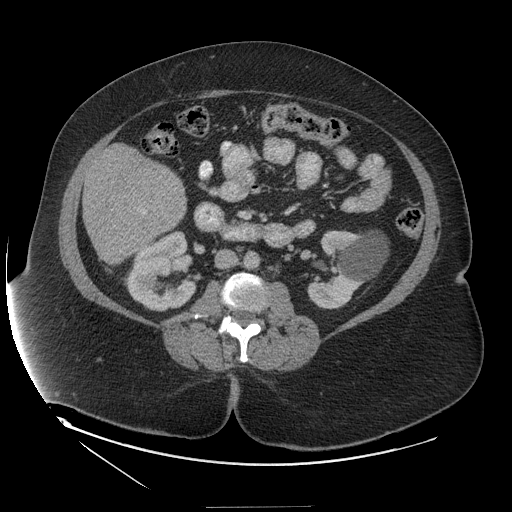
Contrast-enhanced abdominal CT (liver protocol), one axial slice; slice 43 of 127 in the series (ordered by position); reconstruction kernel STANDARD; 140 kVp; soft-tissue window (W 400 / L 40 HU); 2.5 mm slice thickness; 512 × 512 image matrix, field of view 480 × 480 mm. Case-level facts recorded for this patient, not image findings: diagnosis: hepatocellular carcinoma (patient treated with transarterial chemoembolisation; whether this scan precedes or follows treatment is not stated here); TNM stage (as recorded): Stage-II; Child-Pugh class: A; tumour differentiation: well differentiated.
Structures marked on this image (semi-automatic segmentation, software-assisted and operator-edited):
- liver parenchyma outside the tumour (the mass and vessels are separate outlines, so this box may not span the whole liver): bounding box <82,144,186,264> (left, top, right, bottom; pixels)